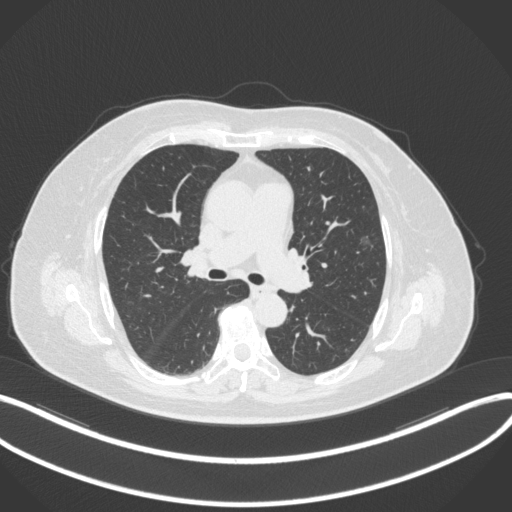
Chest CT, one axial slice. Position 189 of 286 along the scan axis. Reconstruction kernel B31f. 120 kVp. Lung window (W 1500 / L -600 HU). 512 × 512 image matrix, field of view 400 × 400 mm. Female patient, age 76 years. Case-level facts recorded for this patient, not image findings: clinical TNM (as recorded): T1b N0 M0; histopathological grade: G1-2.
Annotated regions visible in this slice (rectangle marked by the reading radiologist):
- lung tumour (recorded histology: adenocarcinoma): bounding box [x1, y1, x2, y2] px = [355, 227, 377, 250]